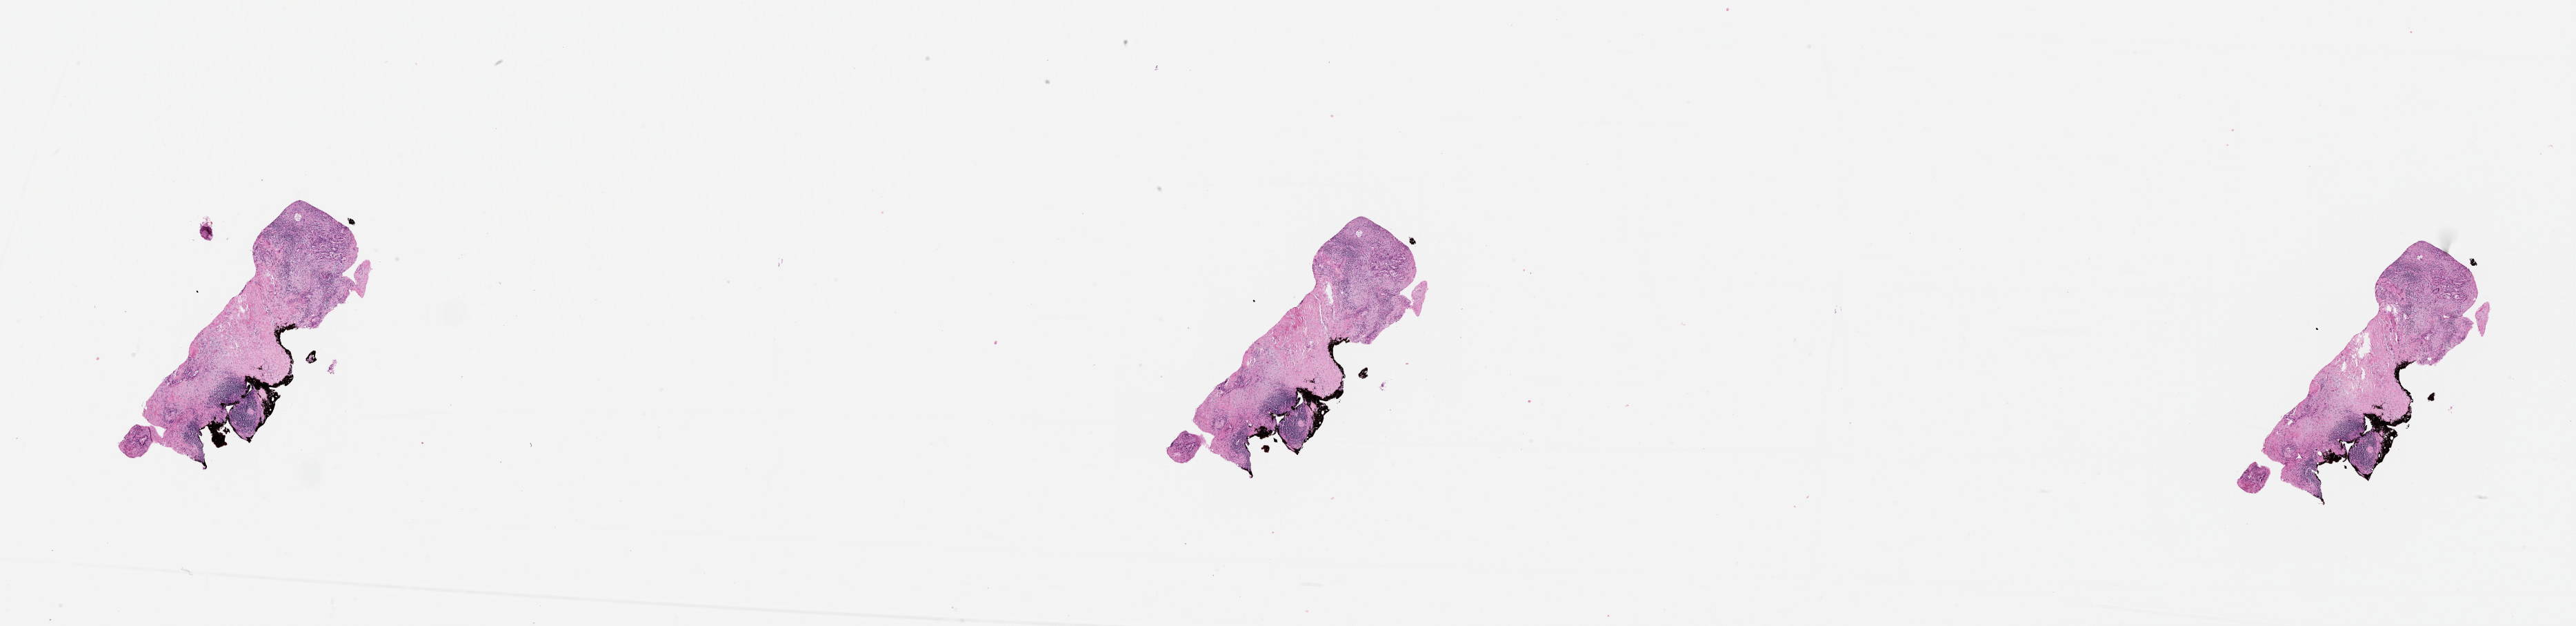
Hematoxylin and eosin (H&E) stained whole-slide image — shown as a low-resolution overview of the whole scanned area (about 30.1 x 7.3 mm). Pancreas, tumour tissue. Patient: female, age 71 years. Histologic grade: G3 (poorly differentiated).
AJCC pathologic stage: IIB. Primary tumour site (as recorded): head. Diagnosis: Infiltrating duct carcinoma, NOS.